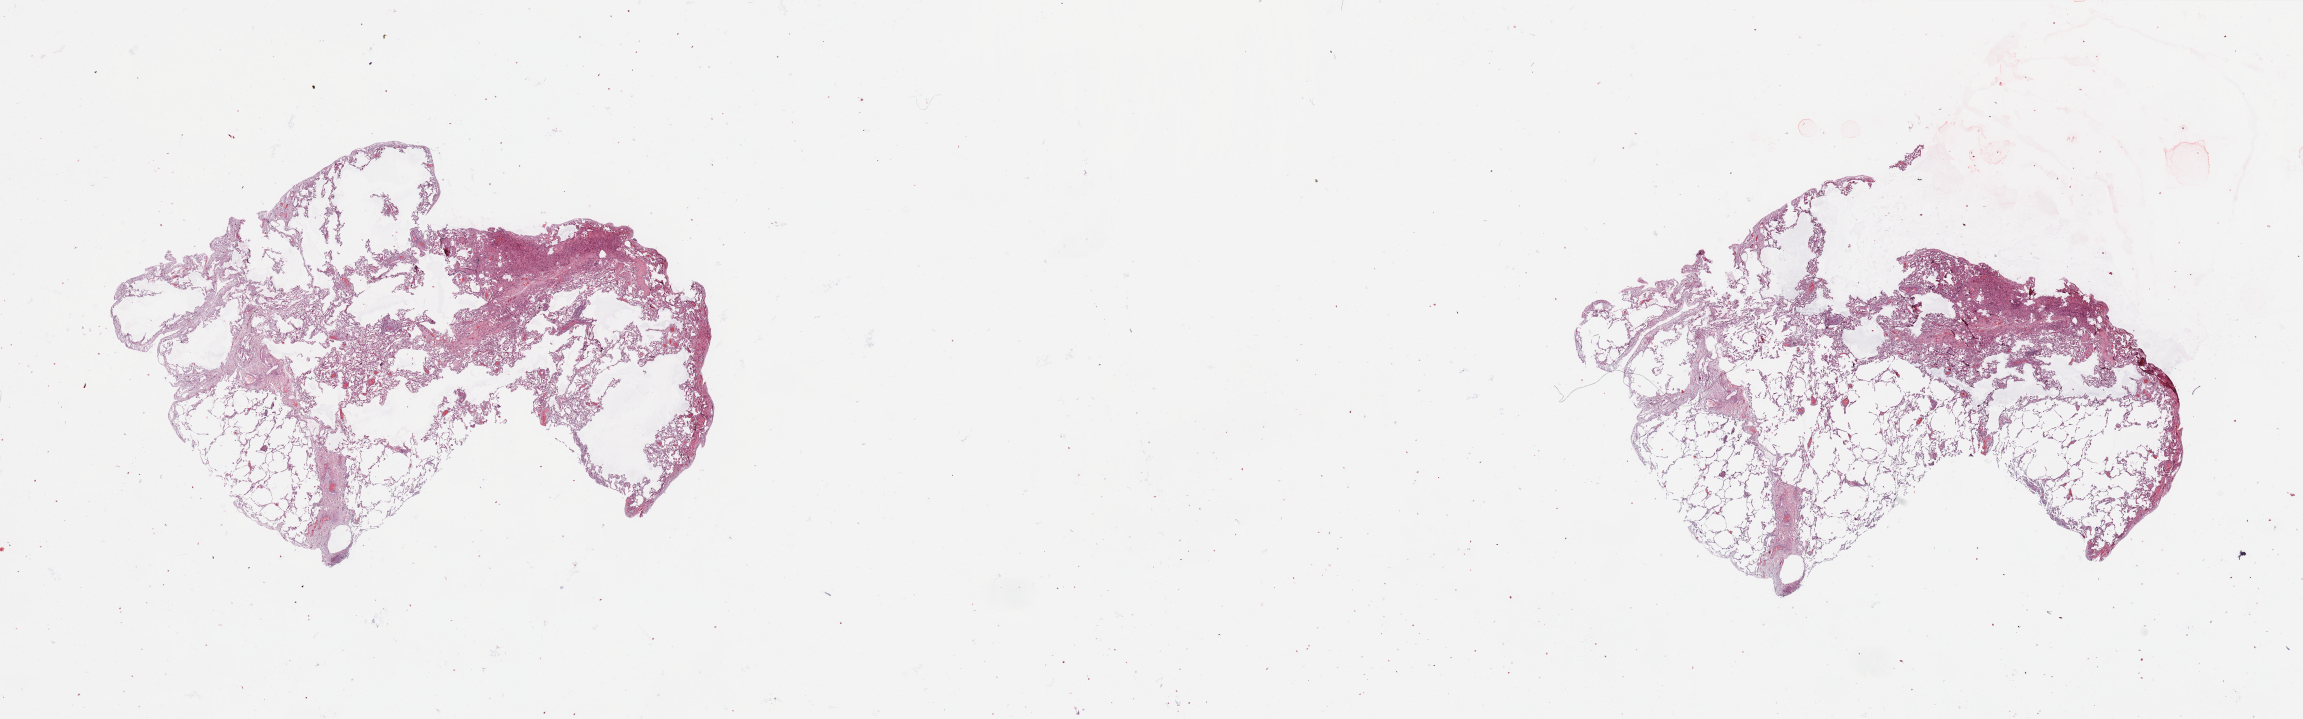
Whole-slide histology image, Hematoxylin and eosin (H&E) stained, low-resolution overview of the scanned area, about 36.4 x 11.4 mm (from a 20x scan); normal (non-tumour) tissue sample, sampled site: lung. 70-year-old female patient.
* this section: normal (non-tumour) tissue from the same patient
* patient diagnosis: Adenocarcinoma, NOS